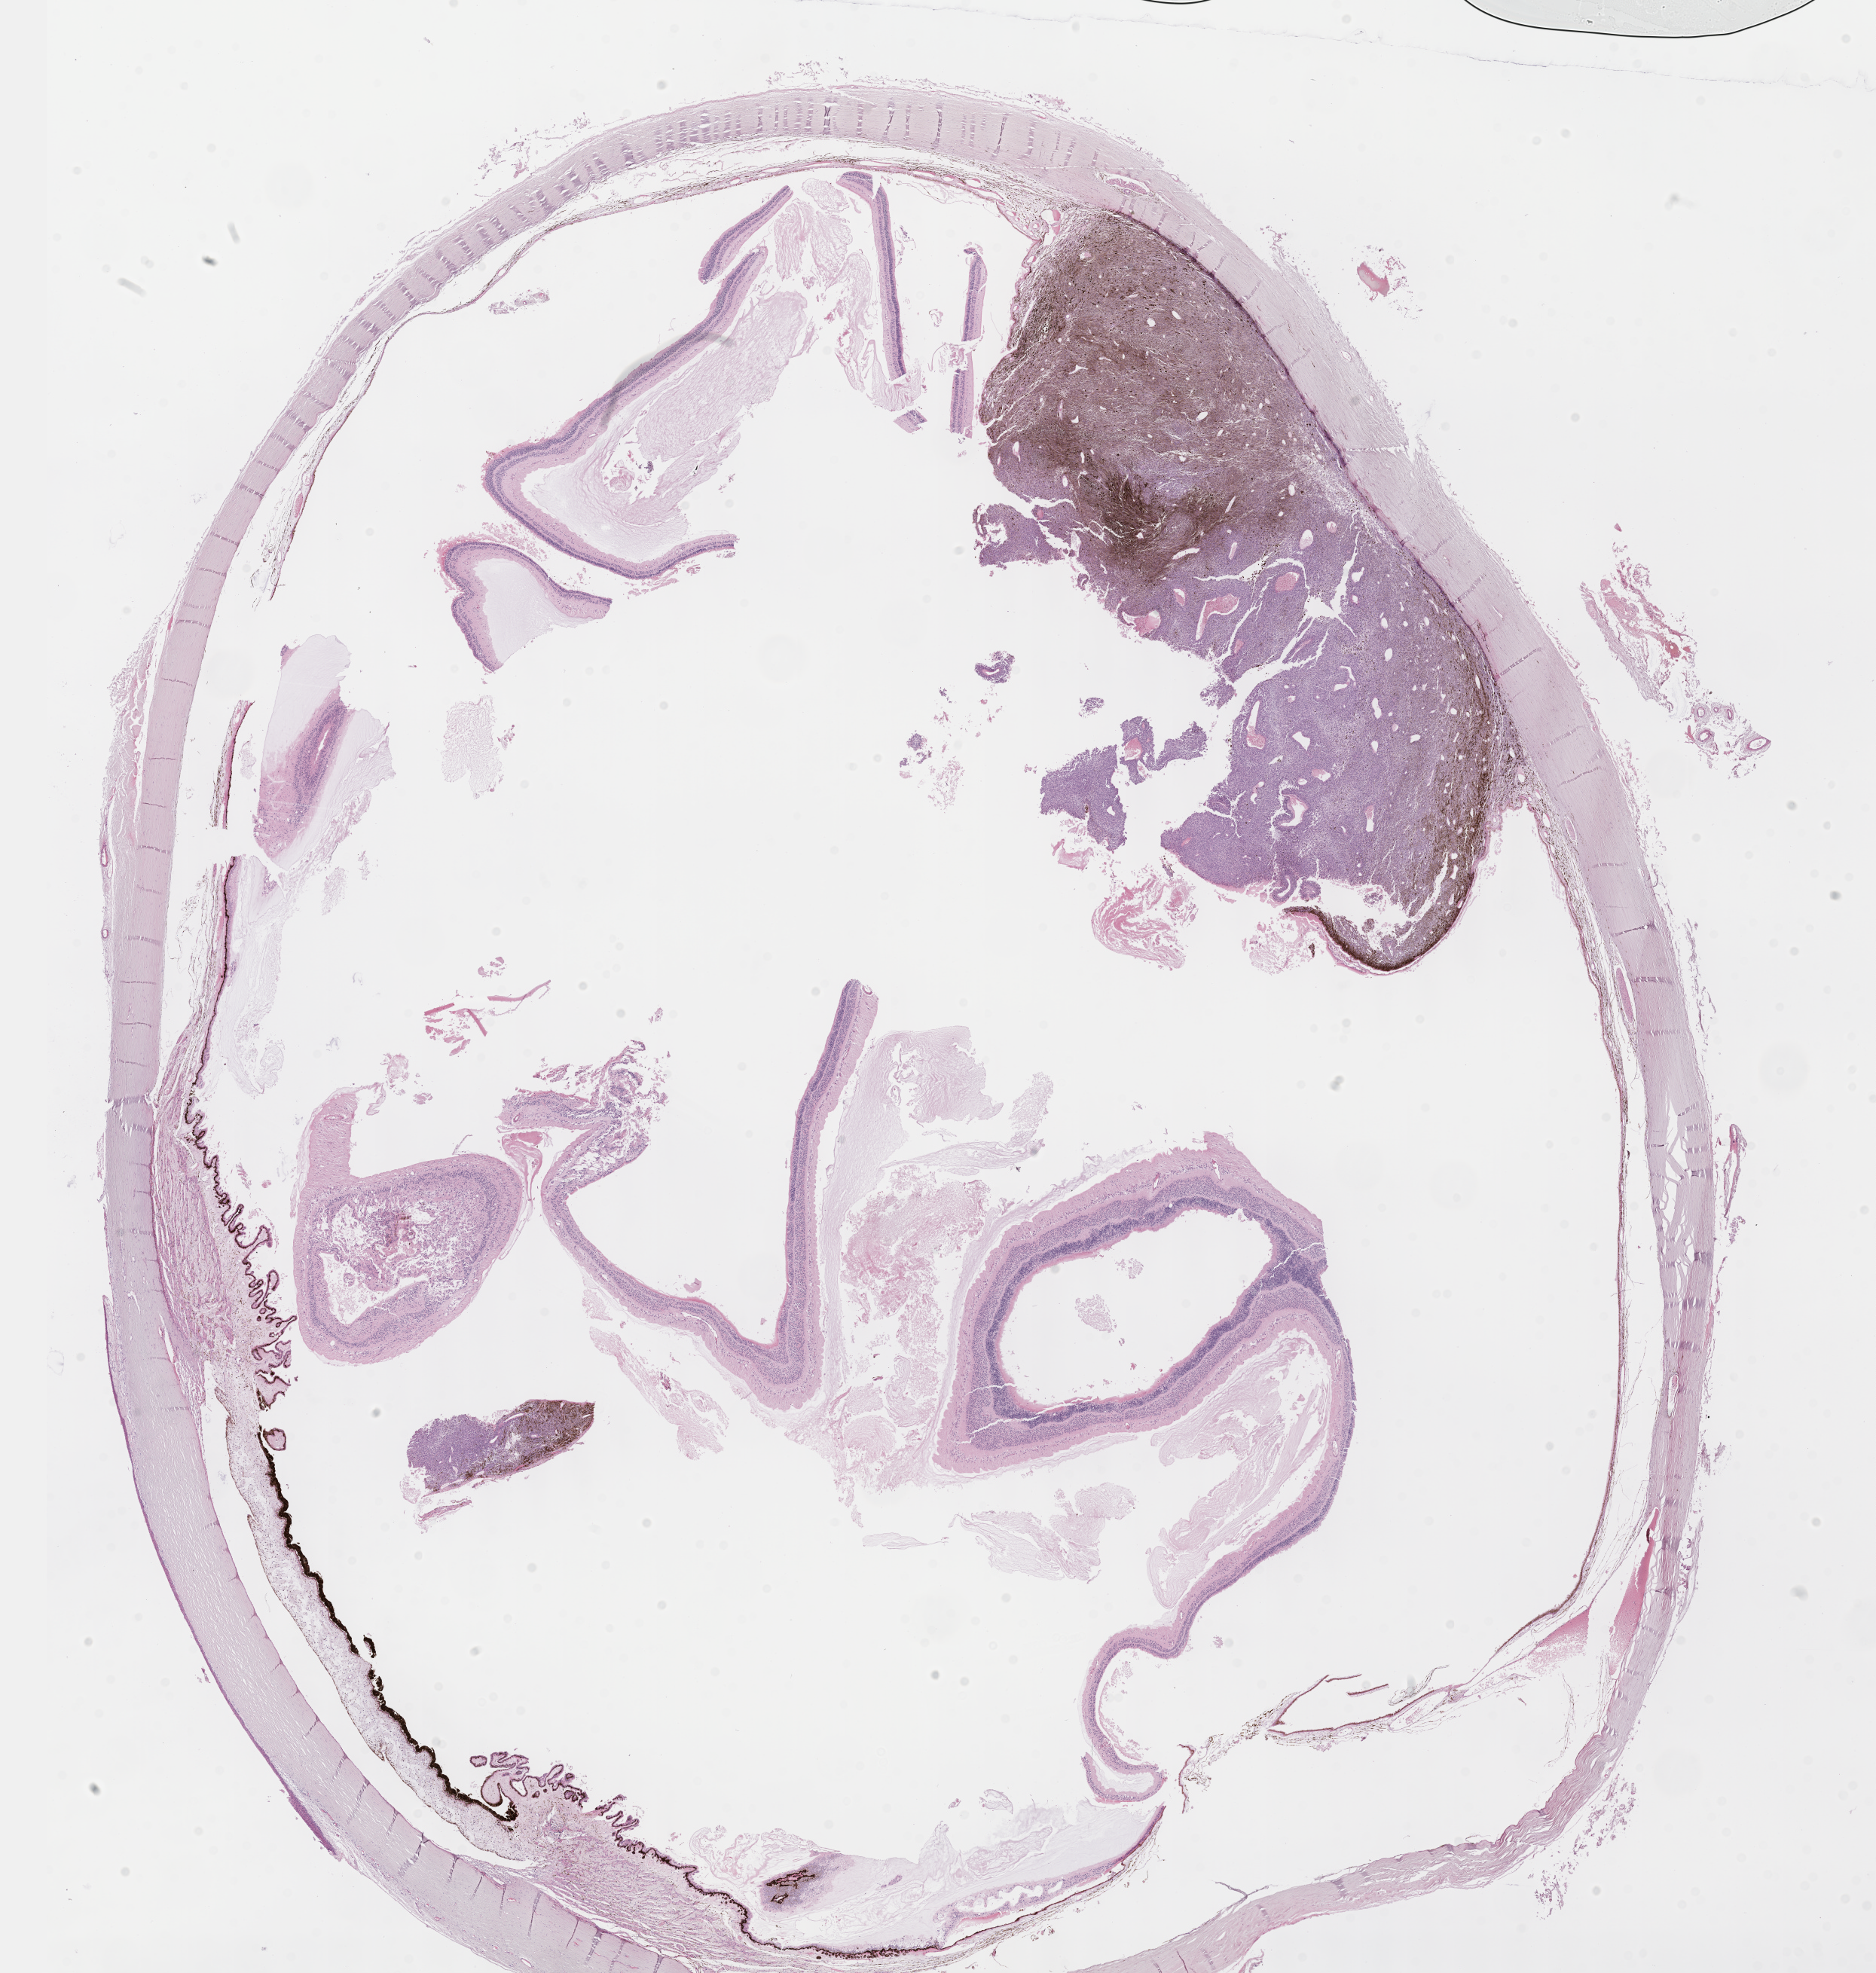
Digitized Hematoxylin and eosin (H&E) stained tissue section (whole slide), low-resolution overview of the scanned area, about 20.1 x 21.2 mm, formalin-fixed paraffin-embedded (FFPE) diagnostic section, uvea, primary tumour sample. Female, age 75 years at initial diagnosis.
Histologic diagnosis: Spindle cell melanoma, NOS (choroid). AJCC pathologic stage: IIB (7th edition).